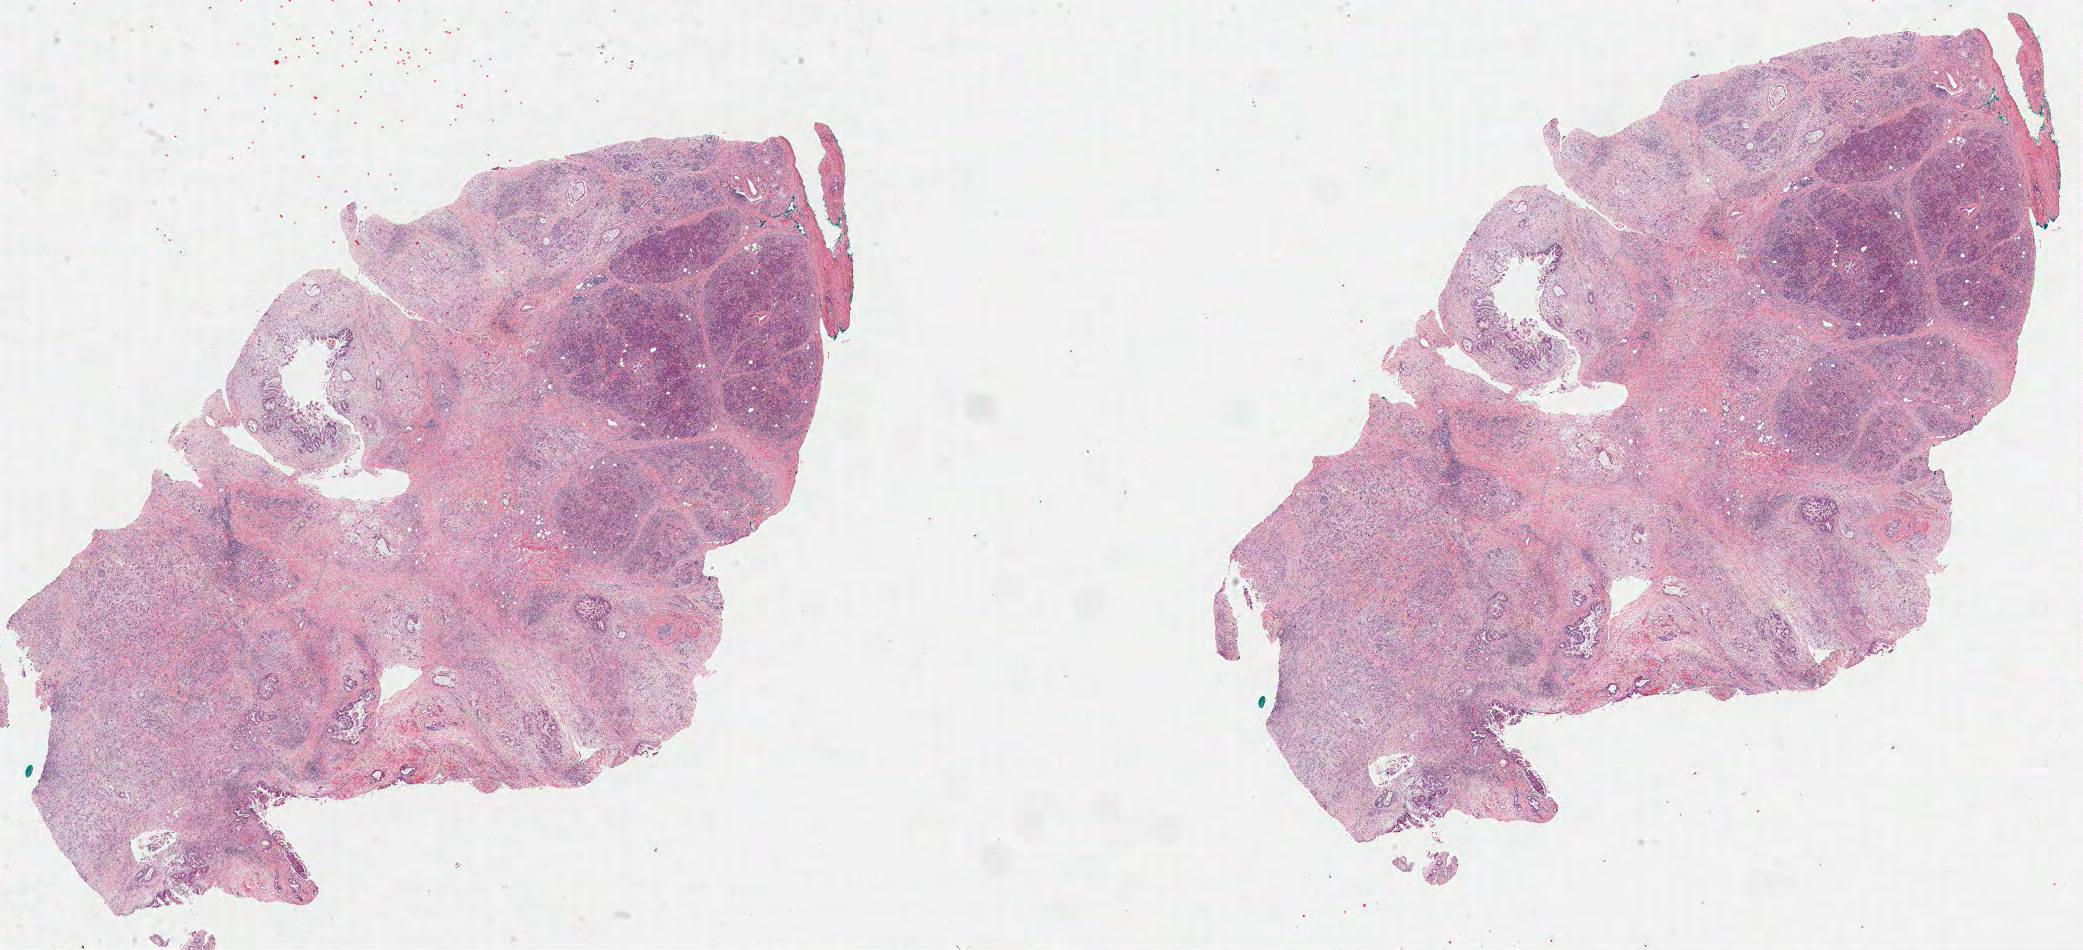
Whole-slide histology image, Hematoxylin and eosin (H&E) stained — shown as a low-resolution overview of the whole scanned area (about 33.6 x 15.3 mm). Formalin-fixed paraffin-embedded (FFPE) diagnostic section. Pancreas, primary tumour sample. Male, age 54 years at initial diagnosis. Histologic grade: G3 (poorly differentiated).
AJCC pathologic stage: IIB (7th edition). Pathologic diagnosis: Adenocarcinoma, NOS. Lymph nodes positive (case pathology): 3 of 32 examined.